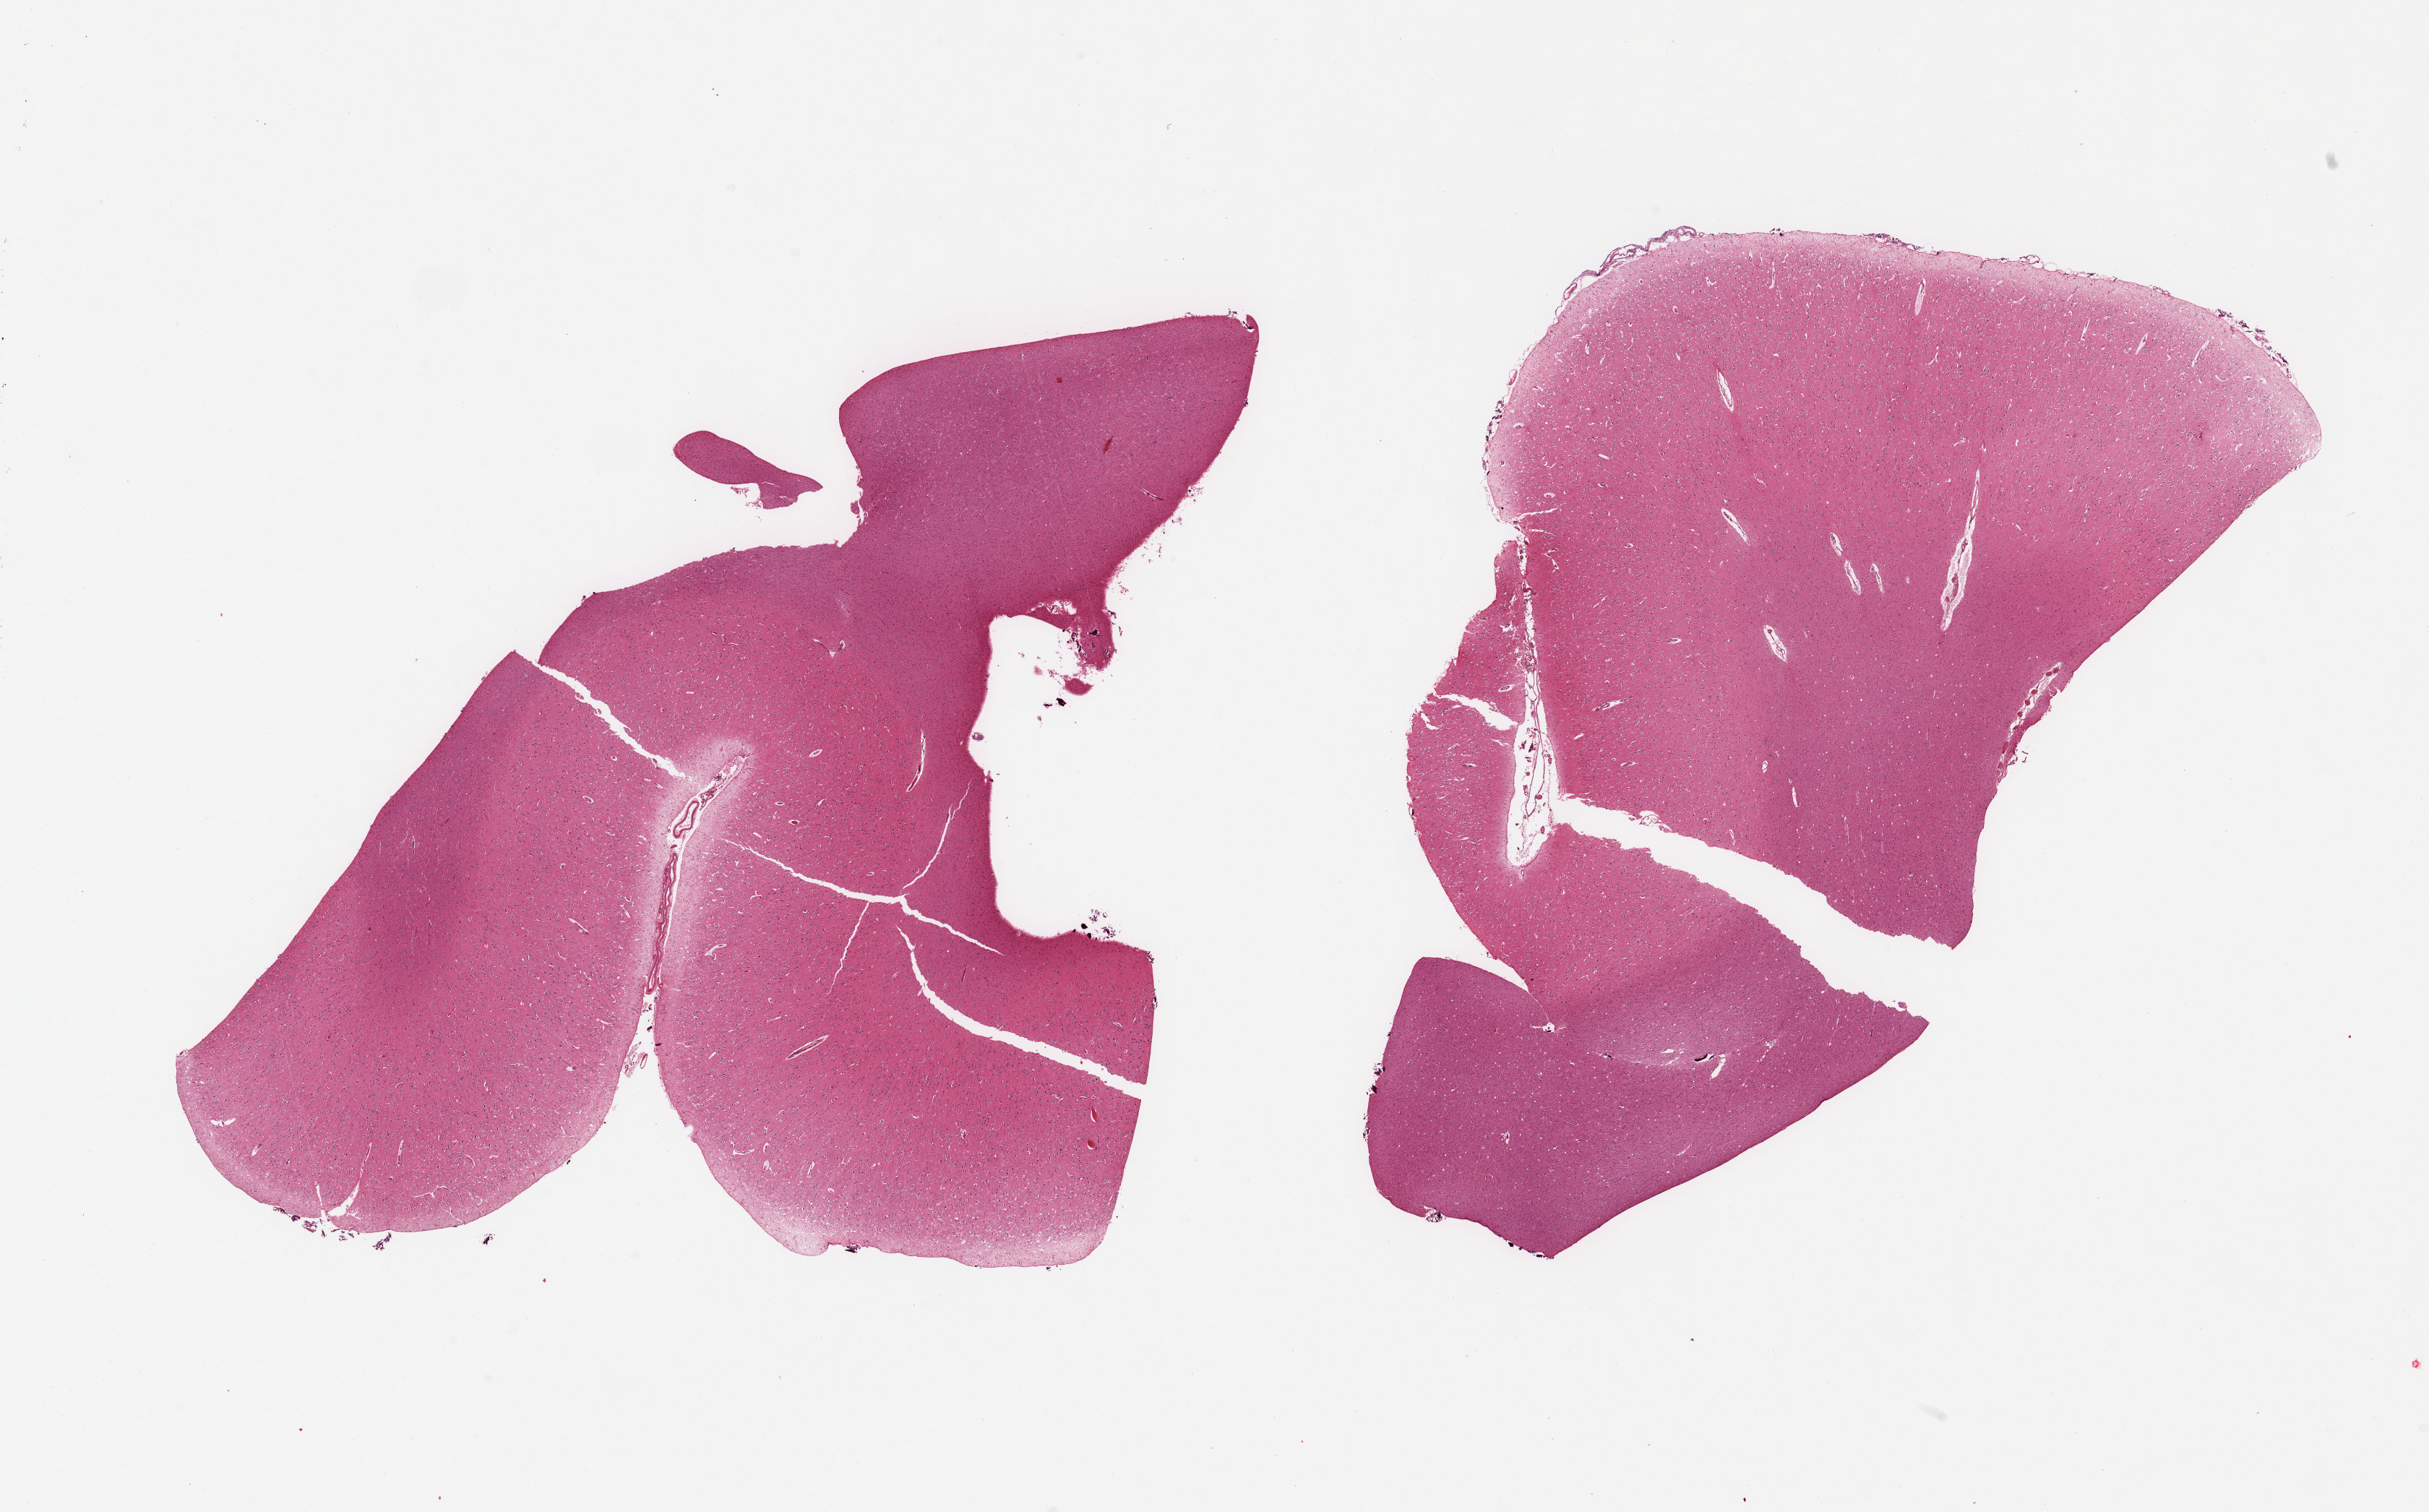
Whole-slide image, haematoxylin and eosin stain, brightfield, whole scanned area (about 26.6 x 16.5 mm, slide scanned at 20x) shown as a low-resolution overview, PAXgene-fixed, paraffin-embedded tissue, section of cerebral cortex (target tissue), donor tissue sample. Donor: male.
Reviewer comment on this tissue sample: 2 pieces.